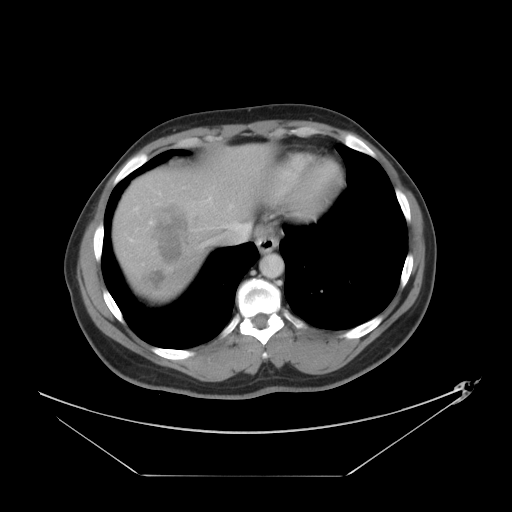
Contrast-enhanced abdominal CT, one axial slice; slice 37 of 44 in the series (ordered by position); 120 kVp; intravenous contrast given; soft-tissue window (W 400 / L 40 HU); 5 mm slice thickness; 512 × 512 image matrix. Male patient, age 49 years. From the clinical record (not read from this slice): diagnosis: colorectal cancer liver metastases, imaged before liver resection; multiple liver metastases: no; largest metastasis: 8.5 cm; disease in both lobes: yes.
Annotated regions visible in this slice (outlined manually by an expert reader):
- hepatic veins: bounding box (x1, y1, x2, y2) in pixels: (135, 207, 252, 243)
- liver: (112, 144, 278, 303)
- planned liver remnant (the part of the liver to remain after resection): (201, 144, 278, 230)
- portal vein (with intrahepatic branches): (150, 221, 153, 224)
- liver metastasis: (142, 205, 187, 287)